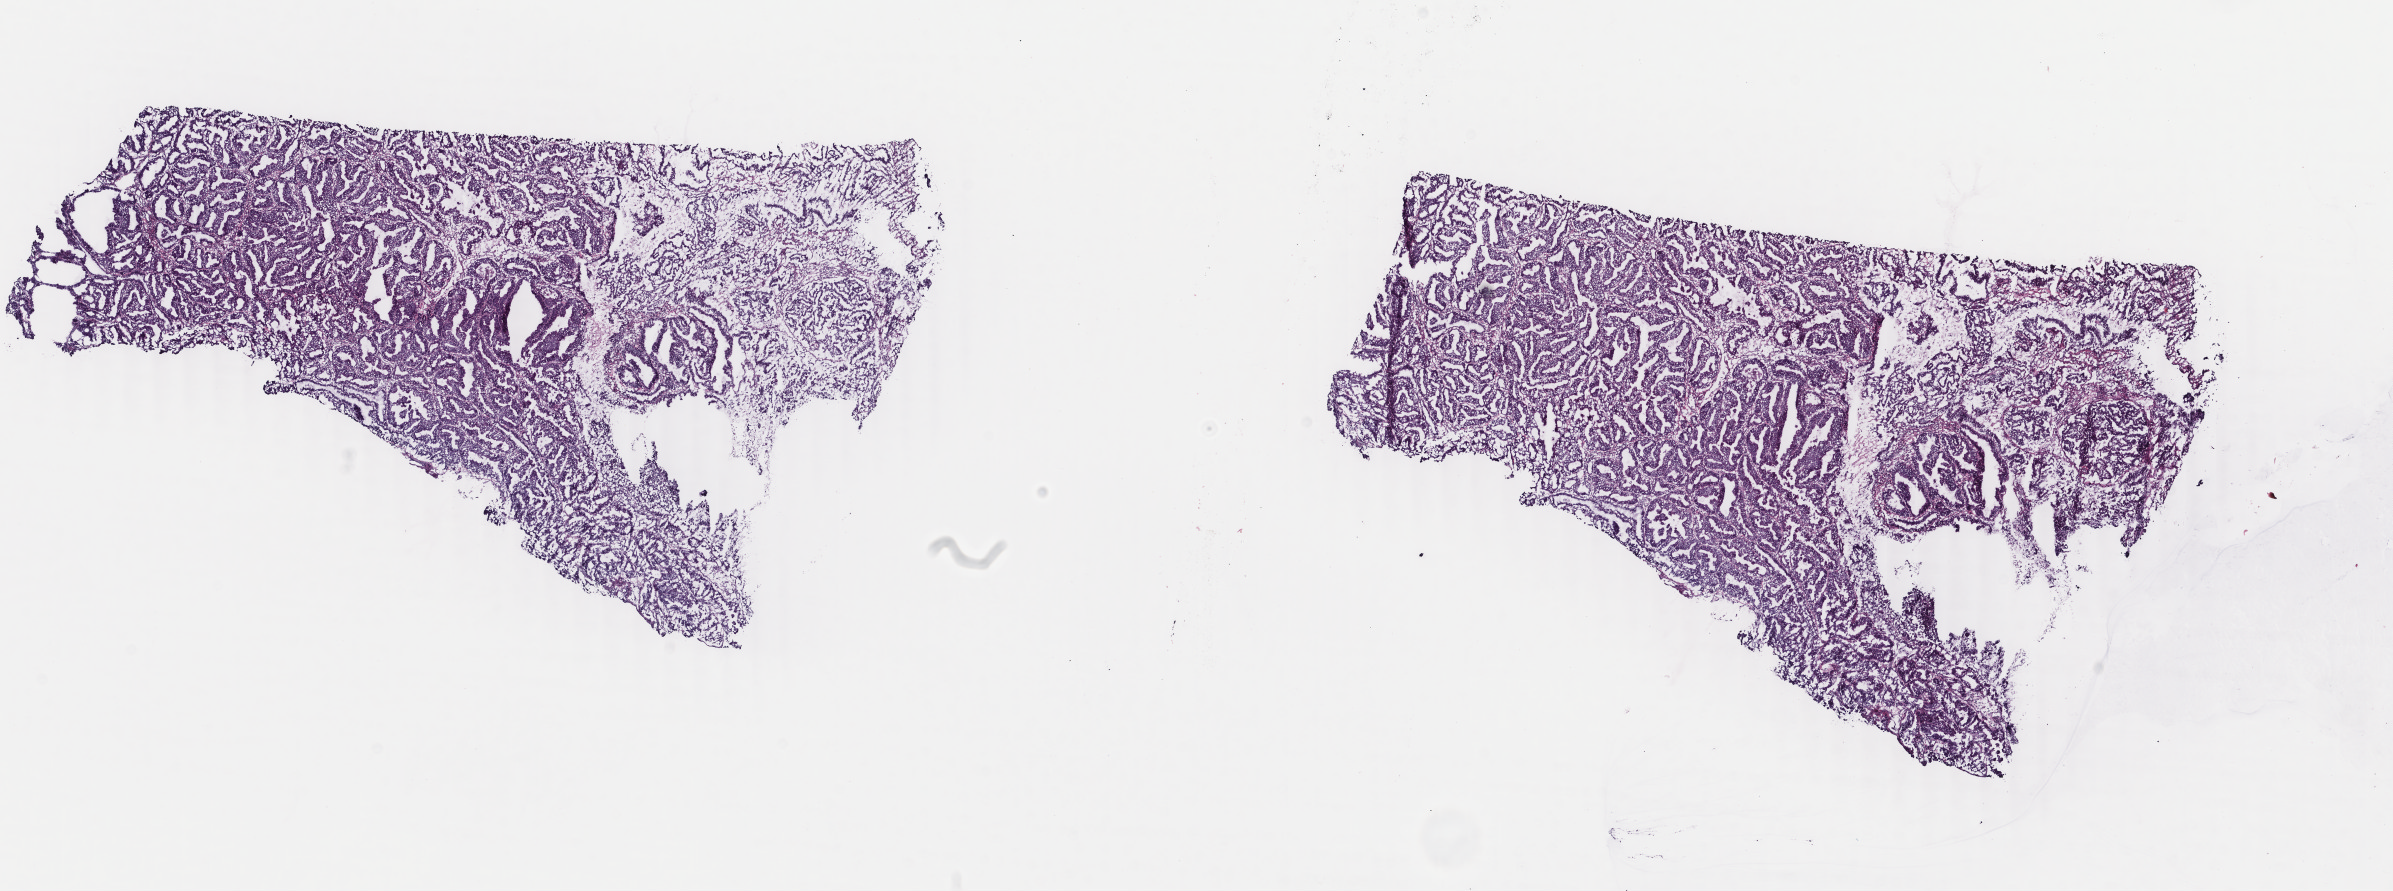
Digitized Hematoxylin and eosin (H&E) stained tissue section (whole slide) — low-resolution overview of the scanned area, about 19.0 x 7.1 mm (slide scanned at 40x), frozen section from the top of the tissue portion, primary tumour sample from the uterus. Female, age 61 years at initial diagnosis. Composition of this section per pathologist review: tumour cells 60%, tumour nuclei 90%.
Histologic diagnosis: Endometrioid adenocarcinoma, NOS (endometrium).